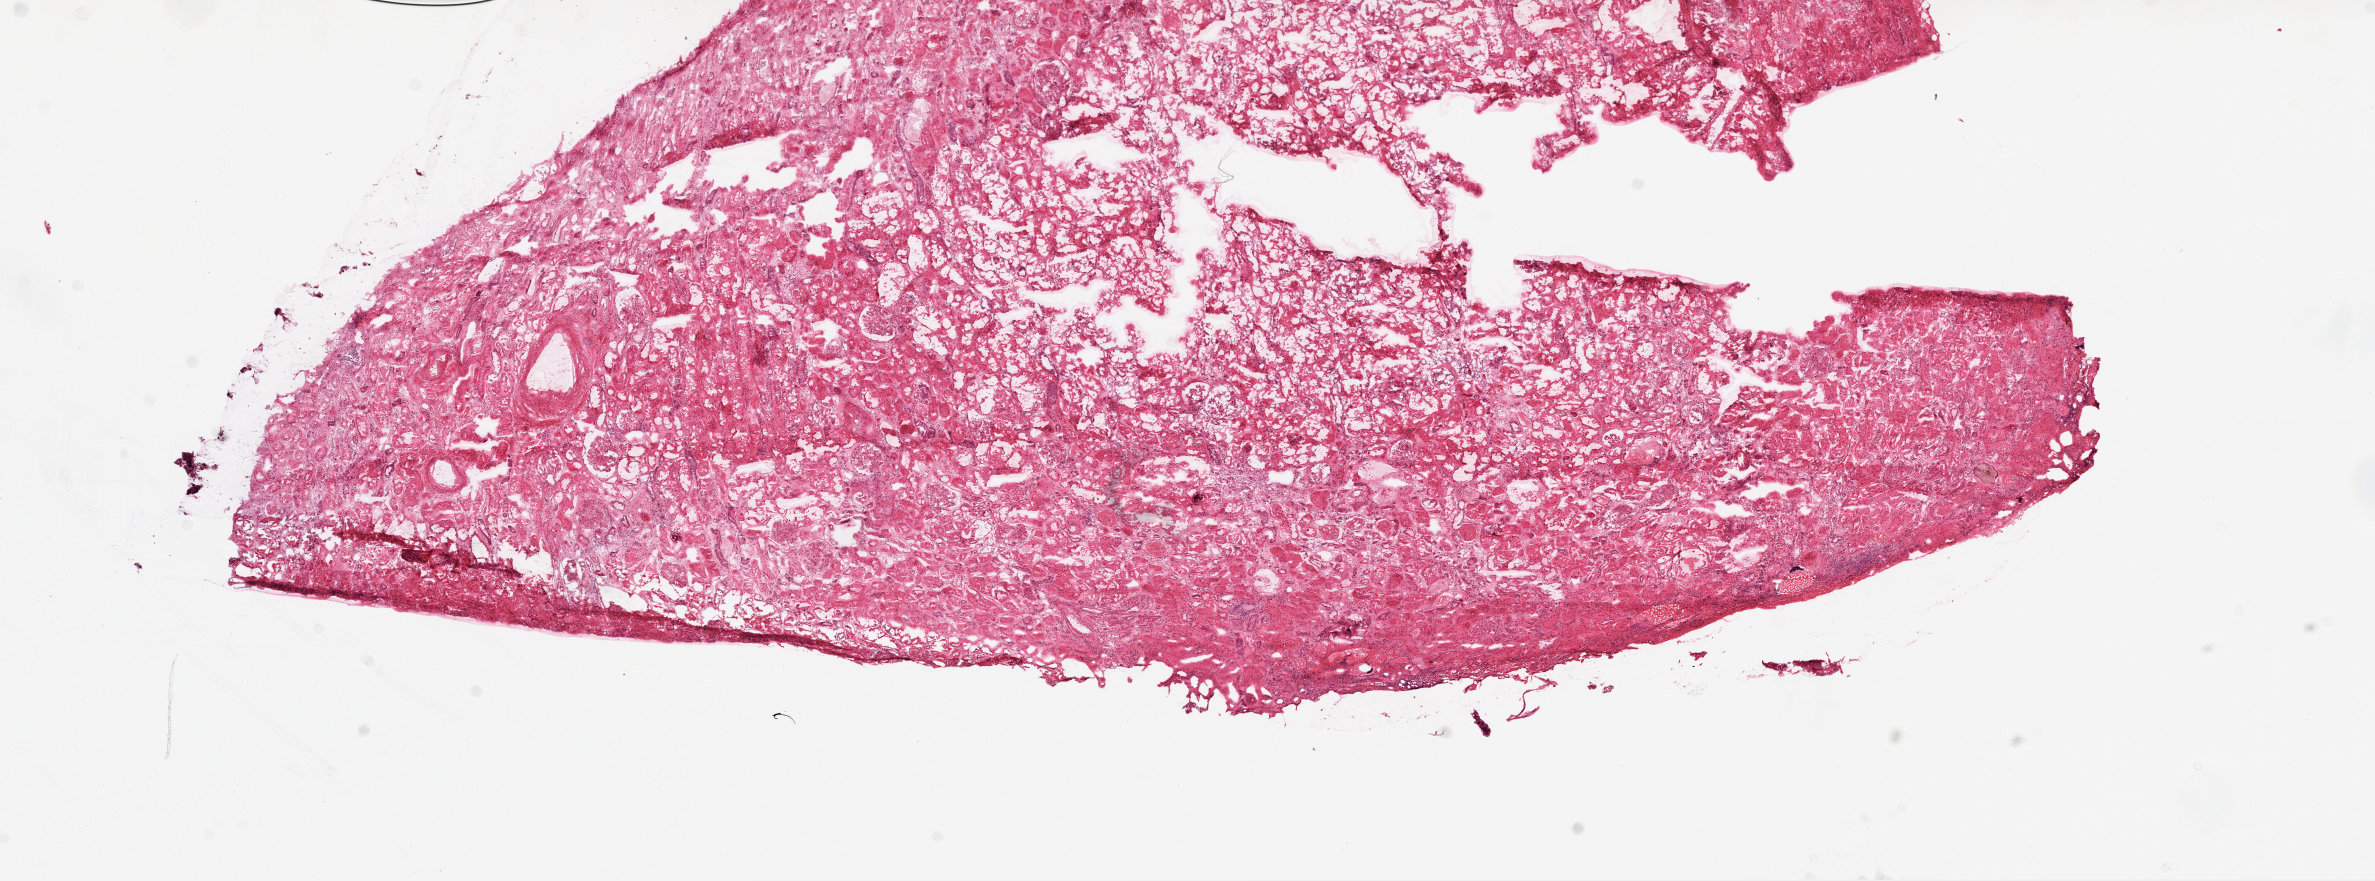
Digitized Hematoxylin and eosin (H&E) stained tissue section (whole slide) — whole scanned area (about 19.1 x 7.1 mm, from a 20x scan) shown as a low-resolution overview, frozen section, sample: solid tissue normal (non-tumour tissue), kidney. Male, age 77 years at initial diagnosis.
• this section: solid tissue normal (non-tumour) sample from the same patient
• patient diagnosis: Clear cell adenocarcinoma, NOS